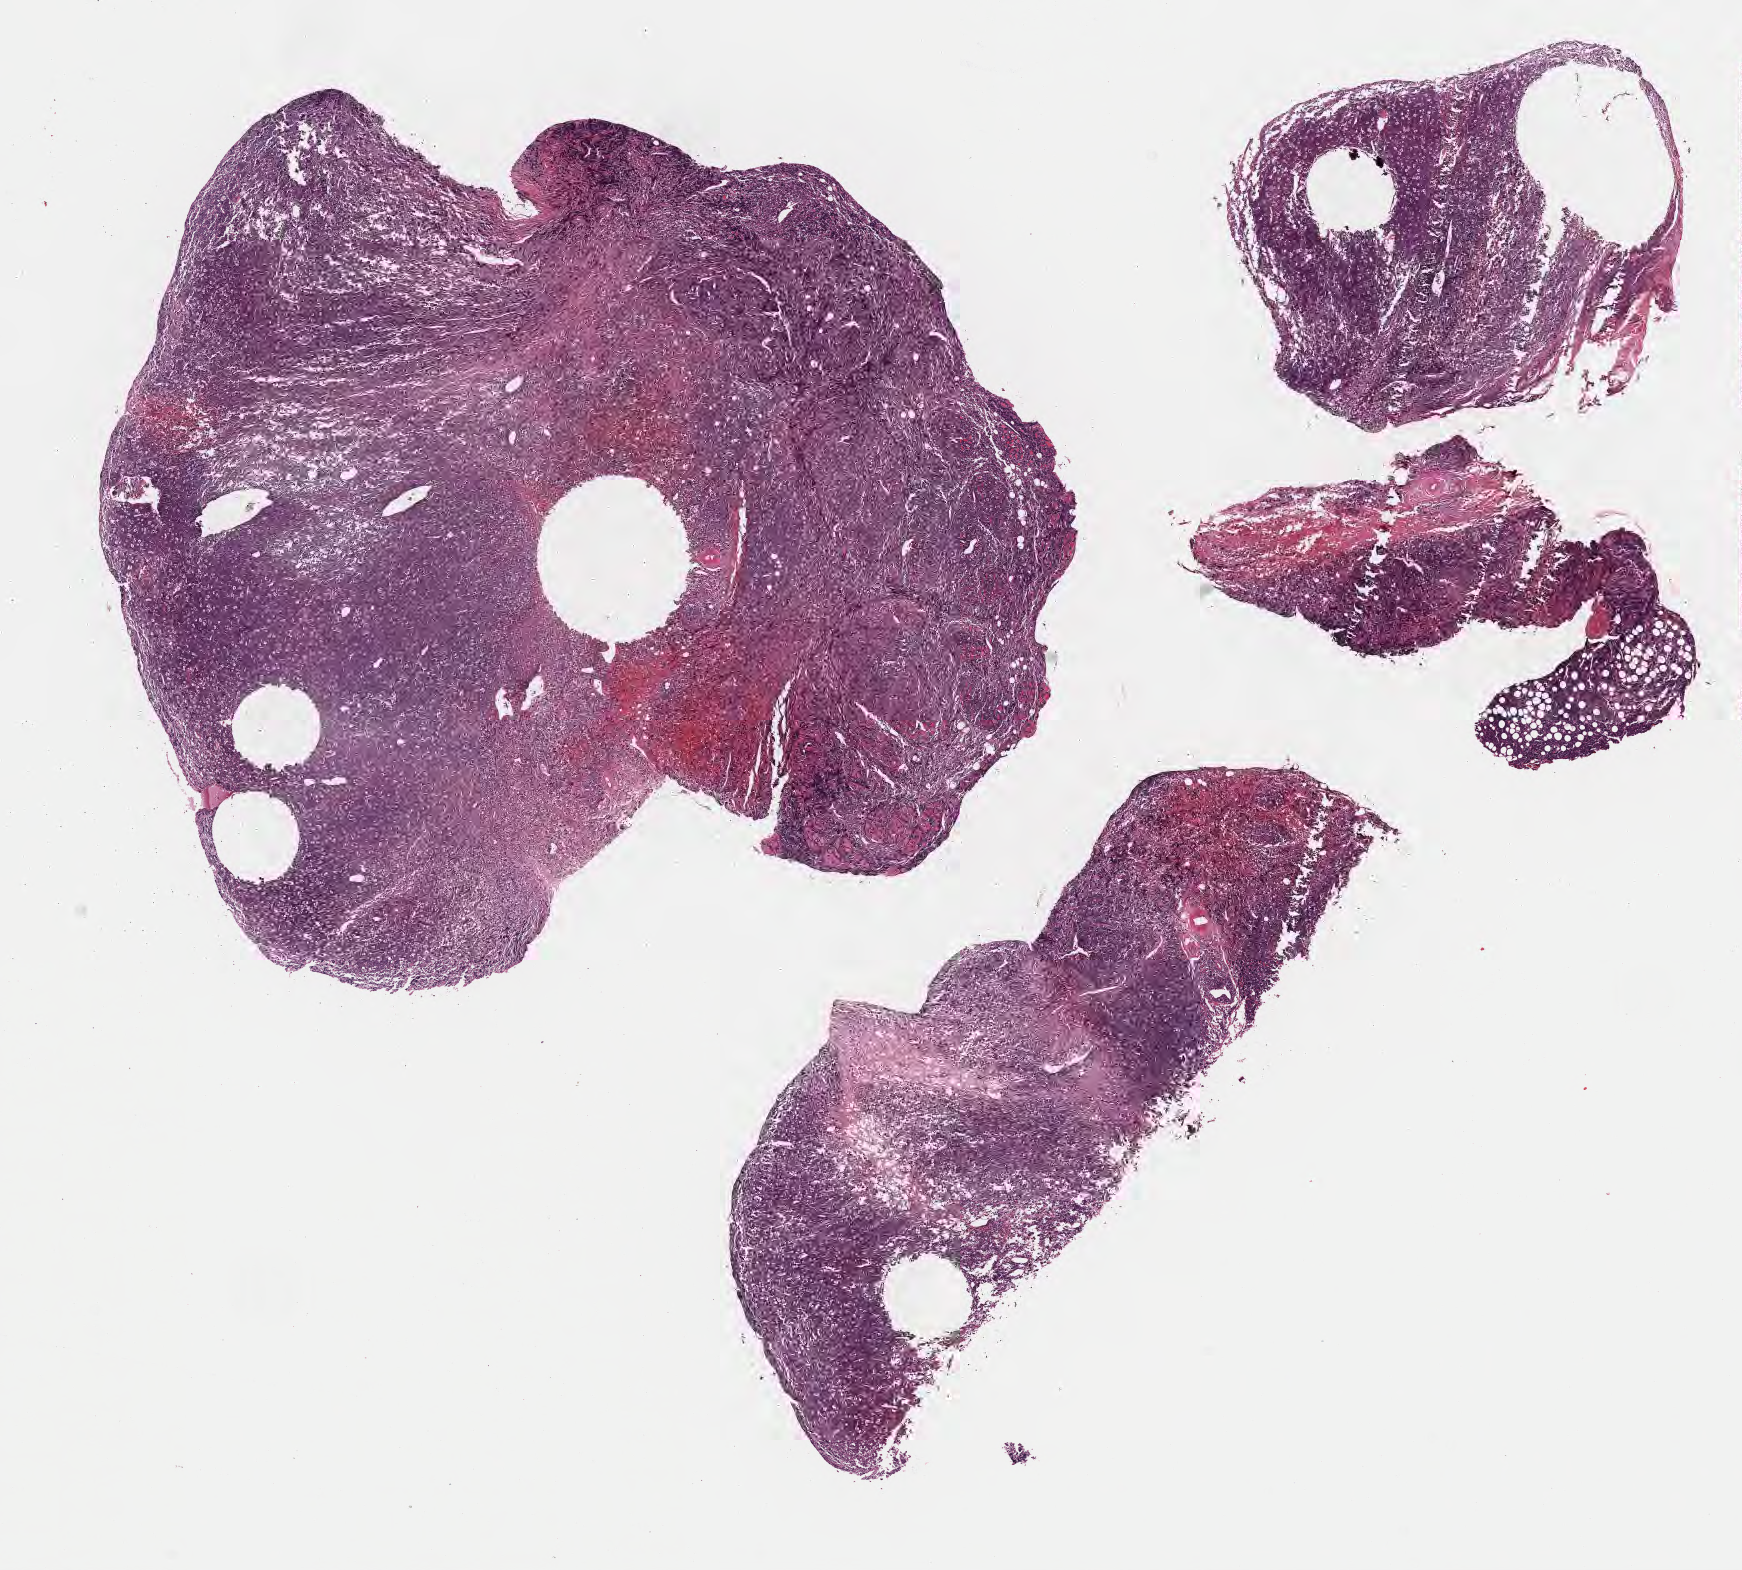
Digitized hematoxylin and eosin (H&E)-stained section — a low-resolution overview of the entire scanned area, about 14.1 x 12.7 mm, formalin-fixed paraffin-embedded section, primary tumor. Patient male; aged 15. Composition of this section per pathologist review: tumor cells 80%, tumor nuclei 85%, stromal cells 15%, necrosis 5%, normal cells 0%. Infiltration values recorded for this section: lymphocyte infiltration 70%, monocyte infiltration 15%, neutrophil infiltration 5%.
* section: bottom of the tissue portion
* histologic diagnosis: Burkitt lymphoma, NOS
* Ann Arbor stage (patient): Stage IV